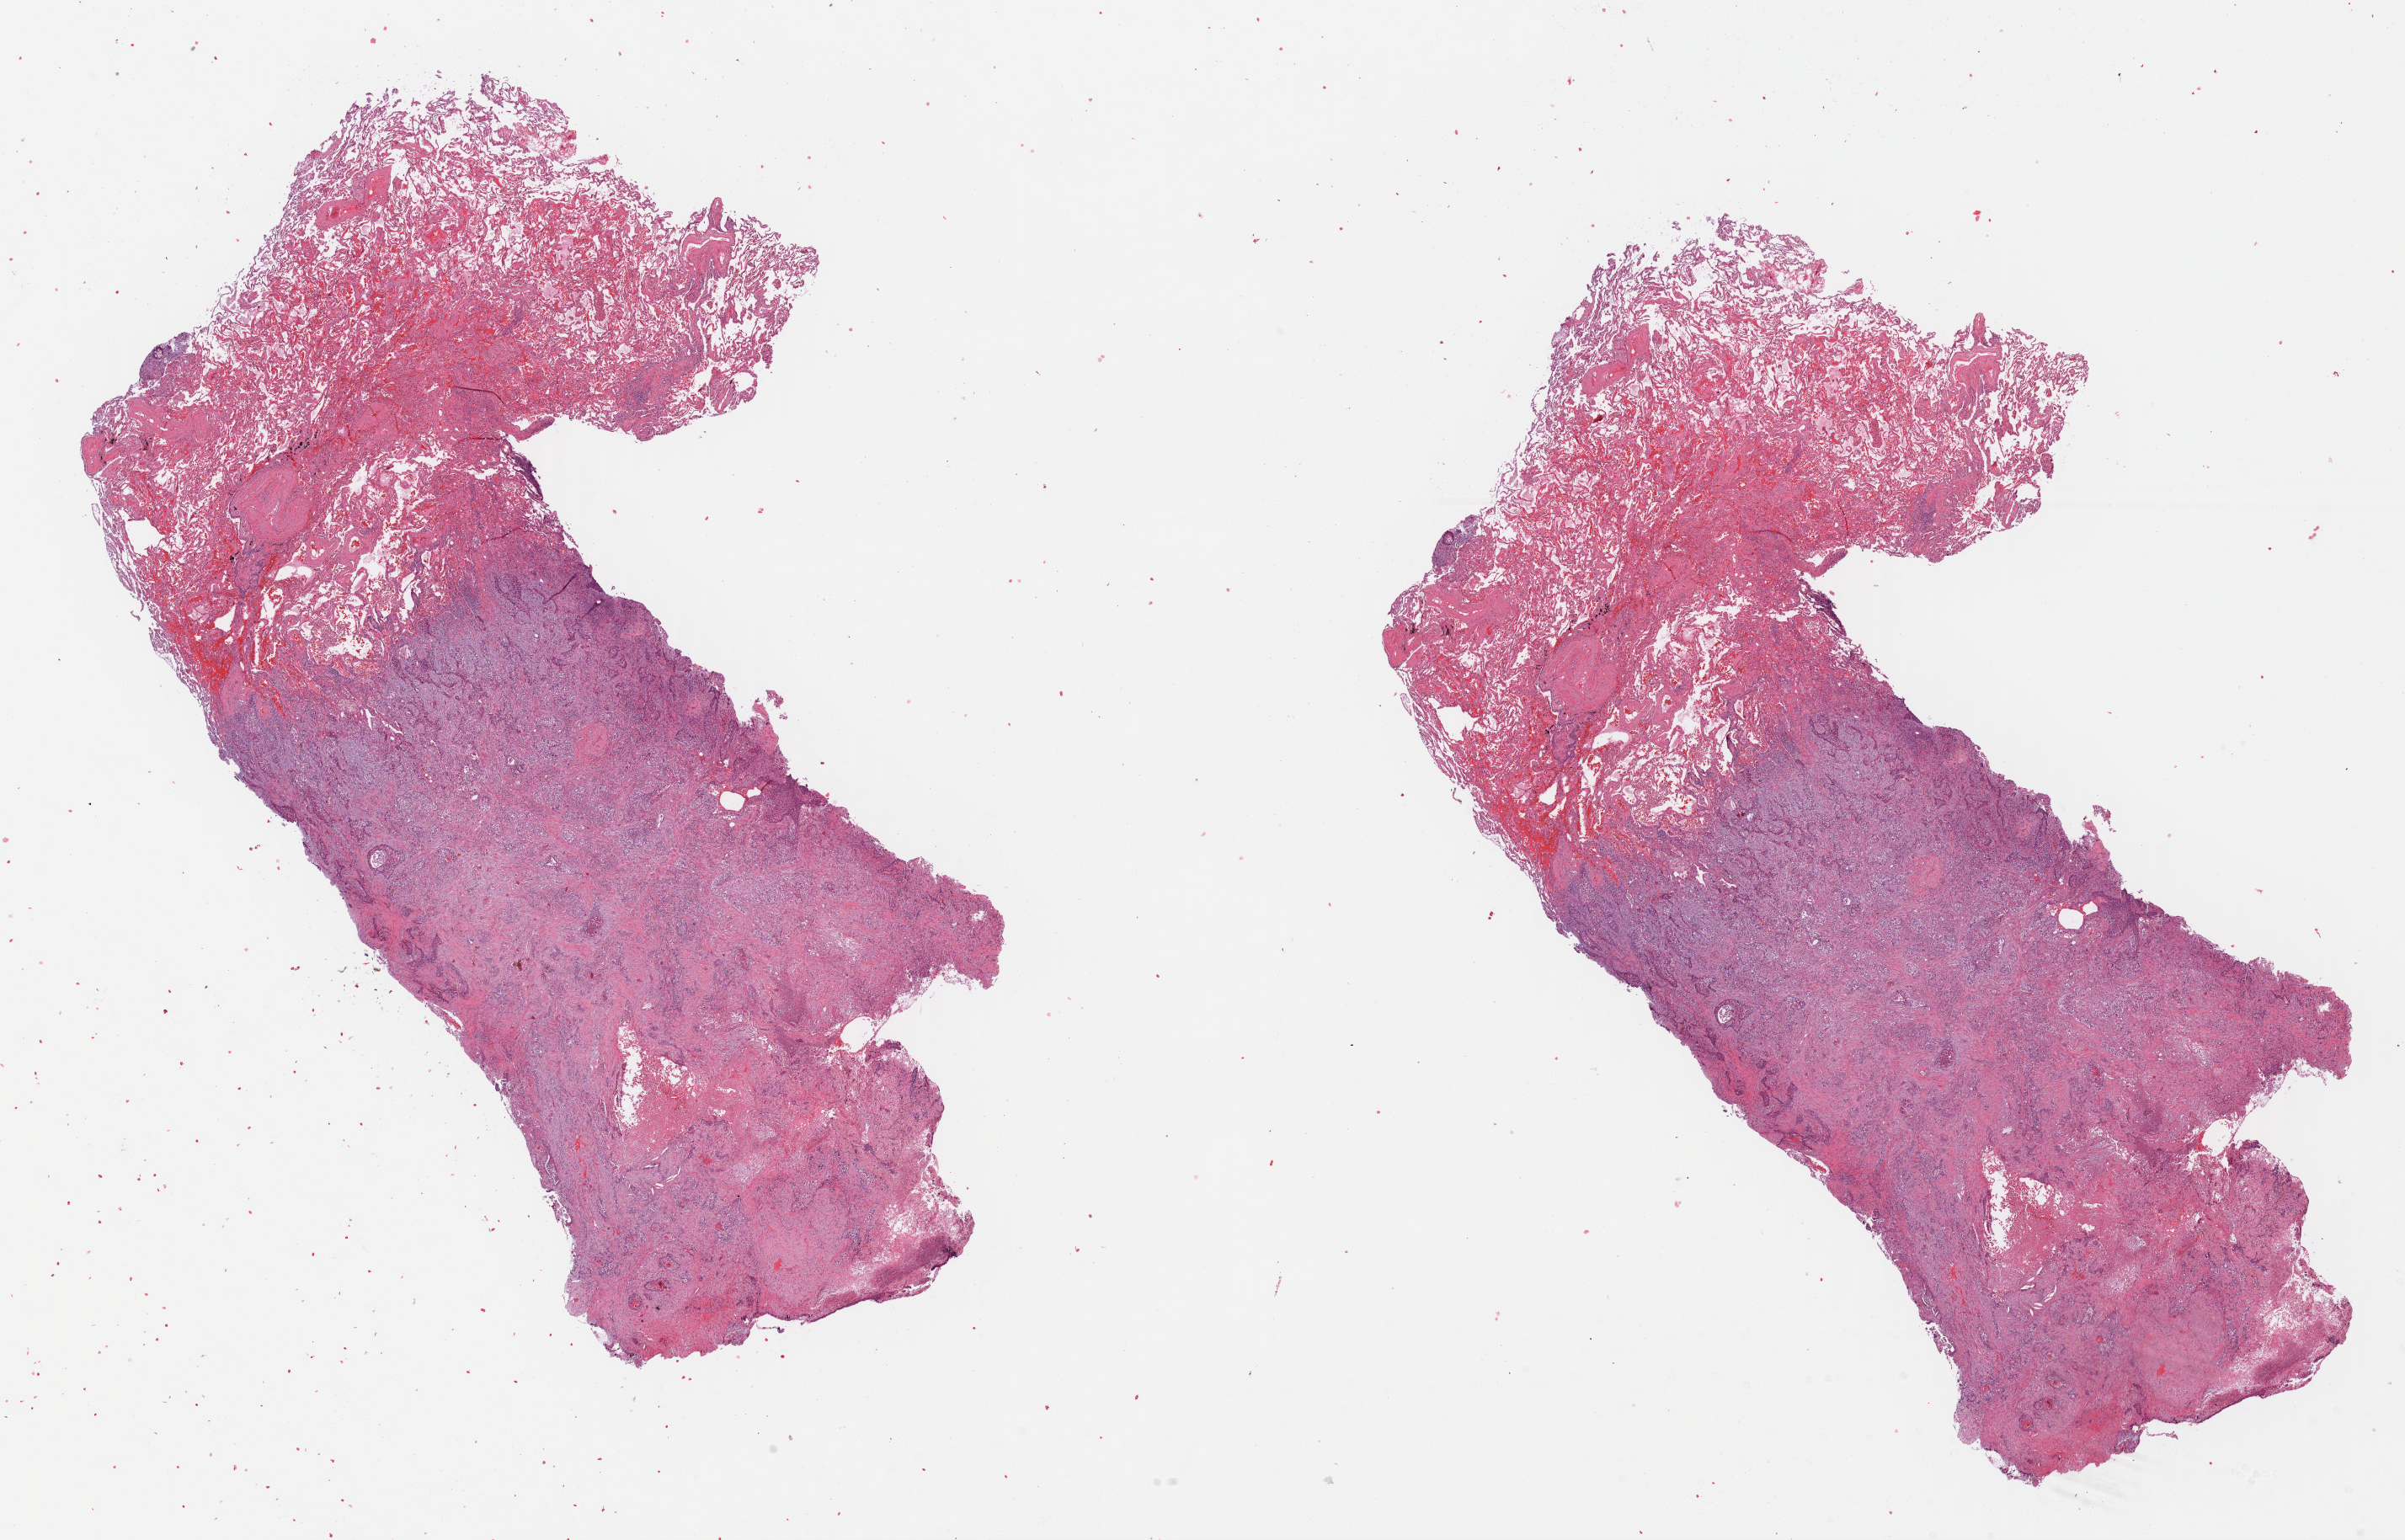
Whole-slide histology image, Hematoxylin and eosin (H&E) stained, shown as a low-resolution overview of the whole scanned area (about 22.4 x 14.4 mm, slide scanned at 40x). Formalin-fixed paraffin-embedded (FFPE) diagnostic section. Primary tumour sample from the lung. Female, age 77 years at initial diagnosis.
Laterality: right. AJCC pathologic stage: IA. Diagnosis: Squamous cell carcinoma, NOS (lower lobe, lung).